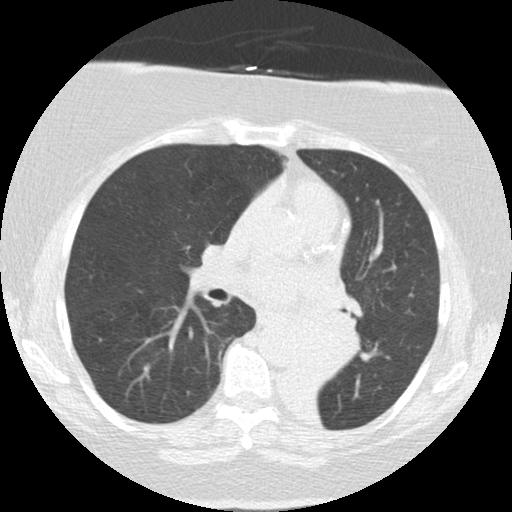
Low-dose screening chest CT, one axial slice; slice 75 of 136 in the series (ordered by position); lung window (W 1500 / L -600 HU); 2.5 mm slice thickness; 512 × 512 image matrix, field of view 309 × 309 mm.
Structures marked on this image (manually delineated by an expert):
- lesion 2 (tumor, mediastinum): box from (x=297, y=310) to (x=361, y=384) px